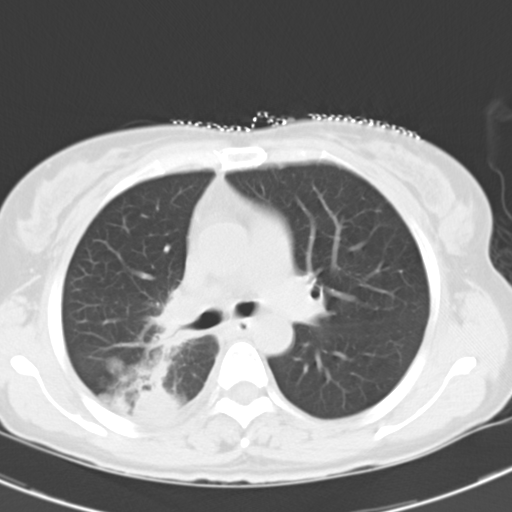
Chest CT, one axial slice; slice 19 of 29 in the series (ordered by position); lung window (W 1500 / L -600 HU); 8 mm slice thickness; 512 × 512 image matrix, field of view 300 × 300 mm. Patient: female, 47 years. From the clinical record (not read from this slice): clinical TNM (as recorded): T1c N3 M0.
Annotated regions visible in this slice (rectangle marked by the reading radiologist):
- lung tumour (recorded histology: adenocarcinoma): bounding box [x1, y1, x2, y2] px = [110, 357, 181, 430]